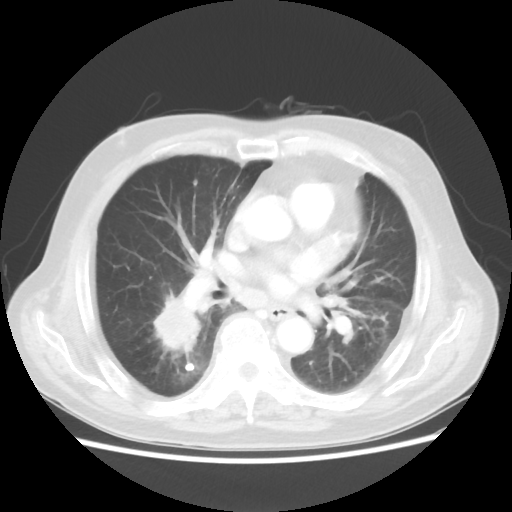
Chest CT, one axial slice; position 20 of 44 along the scan axis; reconstruction kernel STANDARD; 100 kVp; lung window (W 1500 / L -600 HU); 5 mm slice thickness; 512 × 512 image matrix, field of view 359 × 359 mm. Male patient, age 83 years. Case-level facts recorded for this patient, not image findings: clinical TNM (as recorded): T2 N3 M0.
Outlined on this slice (bounding box drawn by a radiologist):
- lung tumour (recorded histology: adenocarcinoma): bounding box (x1, y1, x2, y2) in pixels: (151, 289, 213, 362)